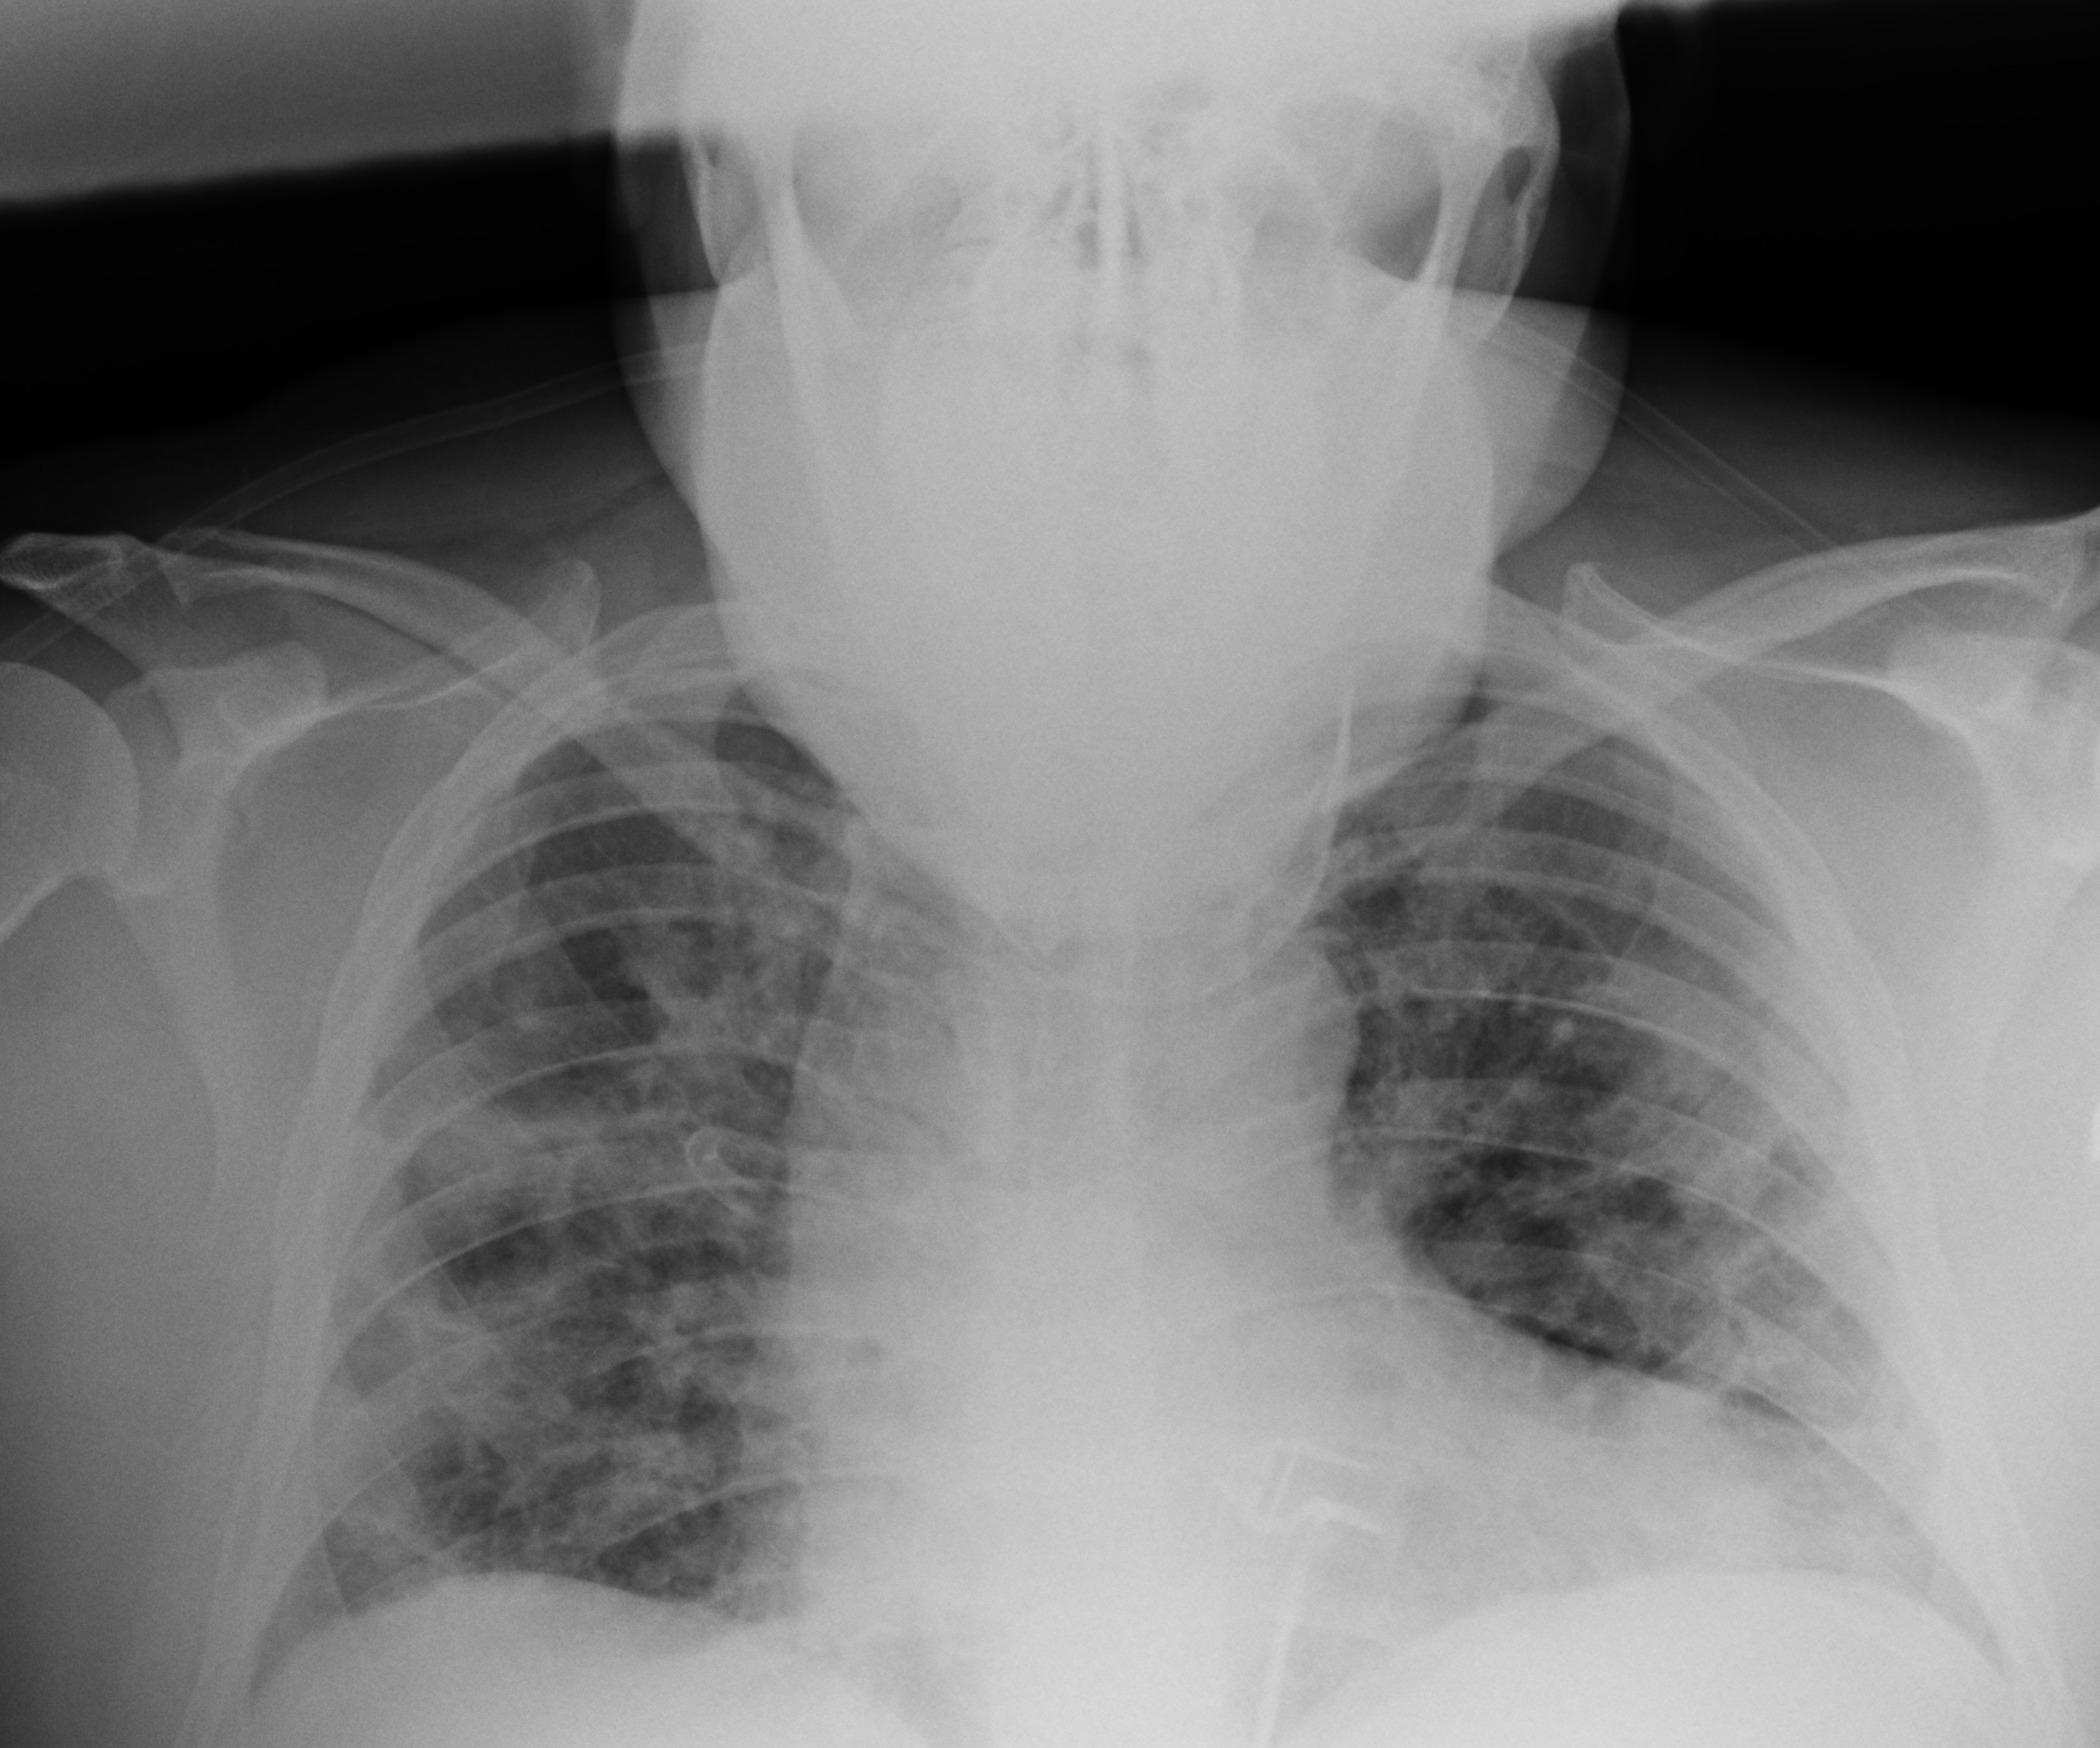
Chest X-ray (portable); anteroposterior (AP) projection. Patient hospitalised with COVID-19; male, aged 18–59 years.
Admission-level facts for this patient (not findings on this image; timing relative to this image not recorded): mechanically ventilated during this hospital stay: no; admitted to intensive care during this hospital stay: no.